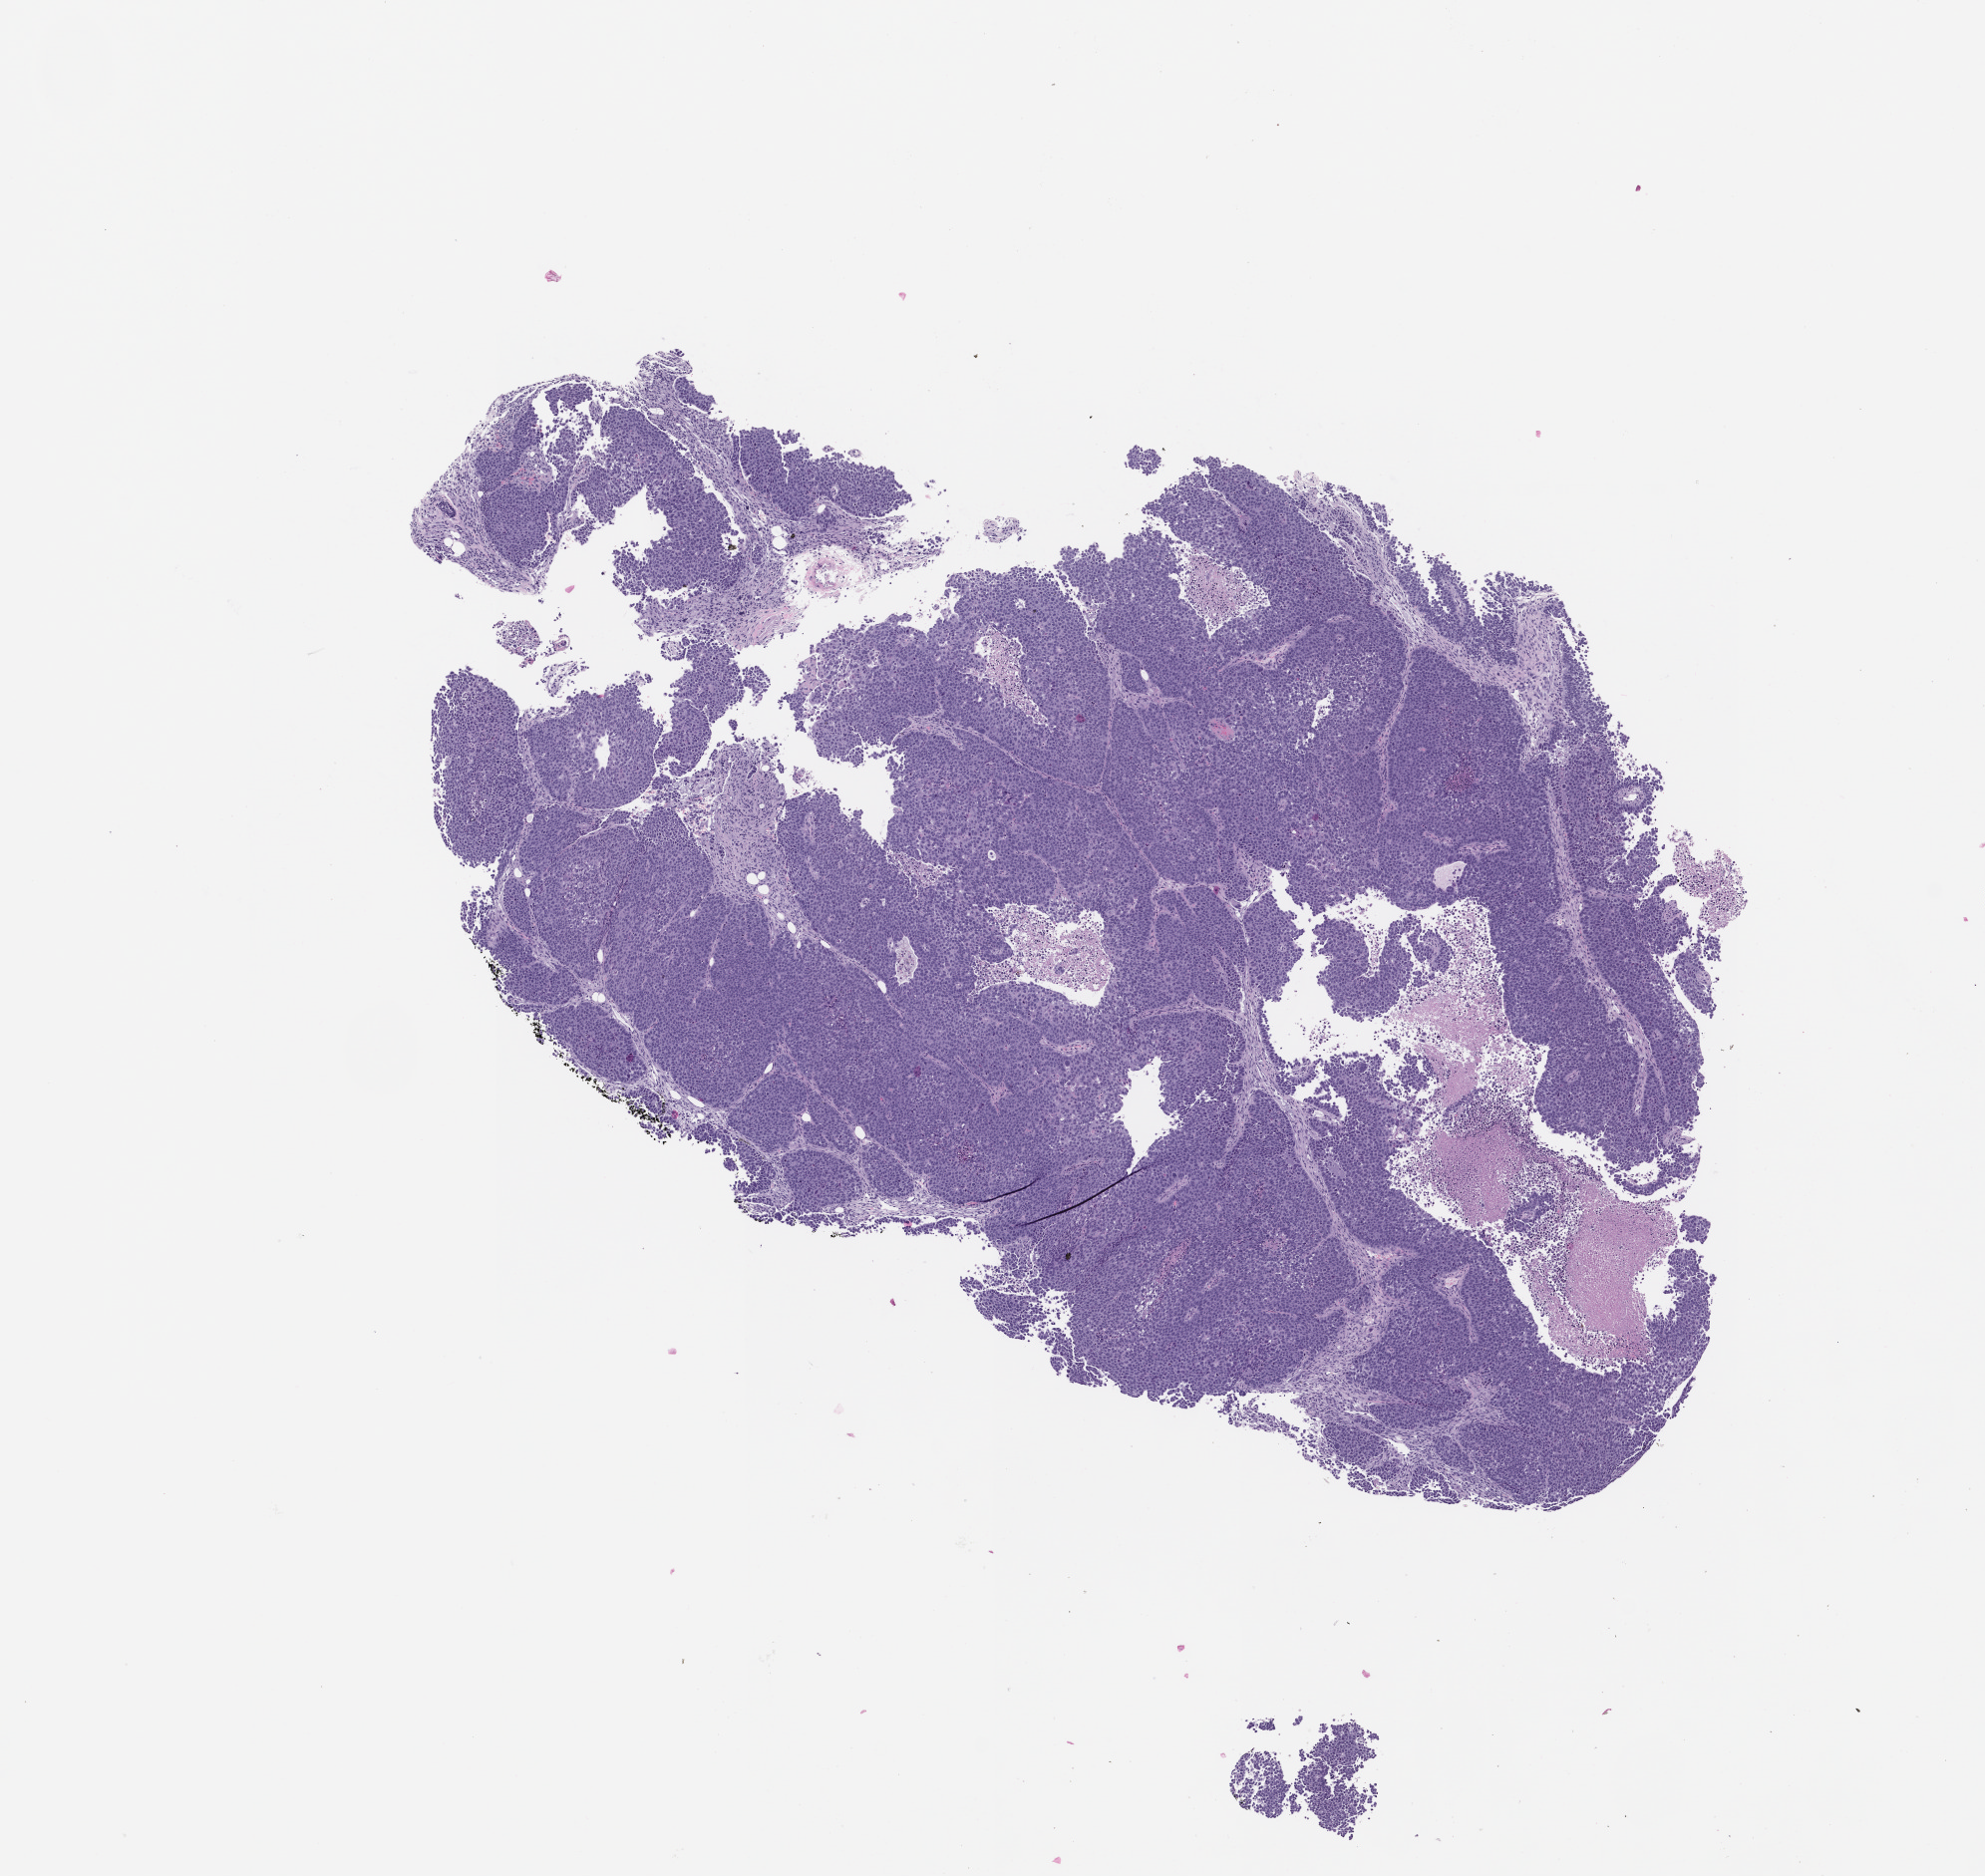
H&E whole-slide image of a patient-derived xenograft (PDX) tumor grown in a mouse, passage 0, whole scanned area (about 8.0 x 7.5 mm) shown as a low-resolution overview. Formalin-fixed, paraffin-embedded (FFPE) tissue. Tumor site category: lung.
Originating patient diagnosis: Lung Squamous Cell Carcinoma.